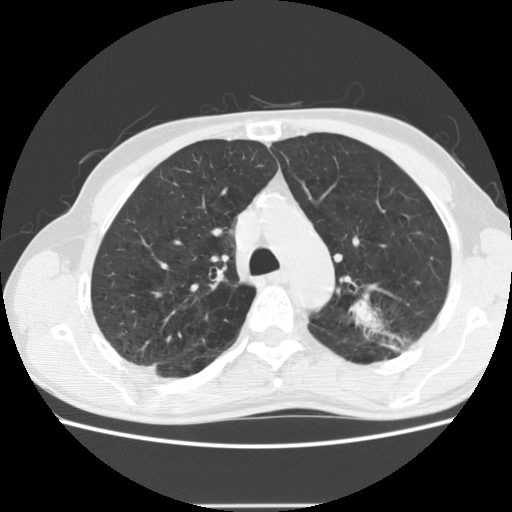
Low-dose screening chest CT, one axial slice. Slice 140 of 191 in the series (ordered by position). 120 kVp. Lung window (W 1500 / L -600 HU). 512 × 512 image matrix, field of view 352 × 352 mm.
Structures marked on this image (expert manual segmentation):
- lesion 1 (tumor, upper lobe of left lung): bounding box [x1, y1, x2, y2] px = [351, 301, 386, 334]